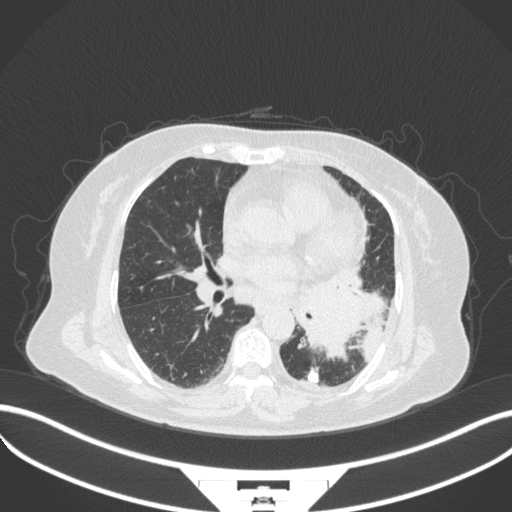
Chest CT, one axial slice; position 171 of 328 along the scan axis; reconstruction kernel B31f; lung window (W 1500 / L -600 HU); 512 × 512 image matrix, field of view 400 × 400 mm. Female patient, age 69 years. From the clinical record (not read from this slice): clinical TNM (as recorded): T2b N3 M1.
Annotated regions visible in this slice (bounding box drawn by a radiologist):
- lung tumour (recorded histology: adenocarcinoma): bounding box [x1, y1, x2, y2] px = [293, 275, 388, 363]